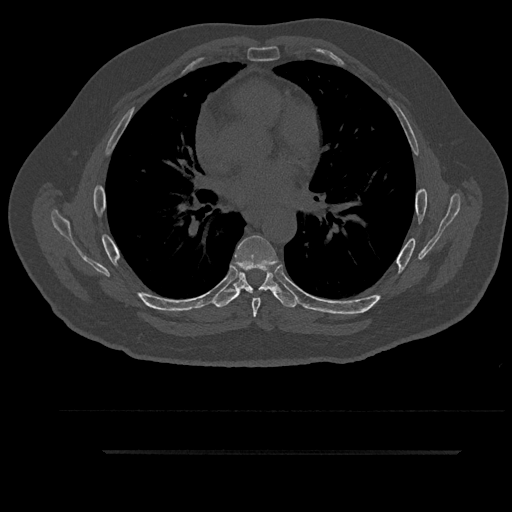
CT including the spine, one axial slice. Position 553 of 797 along the scan axis. Reconstruction kernel Br40s/3. 120 kVp. Bone window (W 1800 / L 400 HU). 0.5 mm slice thickness. 512 × 512 image matrix. Patient: male, 63 years. From the clinical record (not read from this slice): primary cancer: renal.
Annotated regions visible in this slice (semi-automatically segmented with operator editing):
- T5 vertebra: bounding box [x1, y1, x2, y2] px = [260, 287, 266, 290]
- T6 vertebra: [234, 235, 279, 317]
- T7 vertebra: [213, 269, 299, 308]